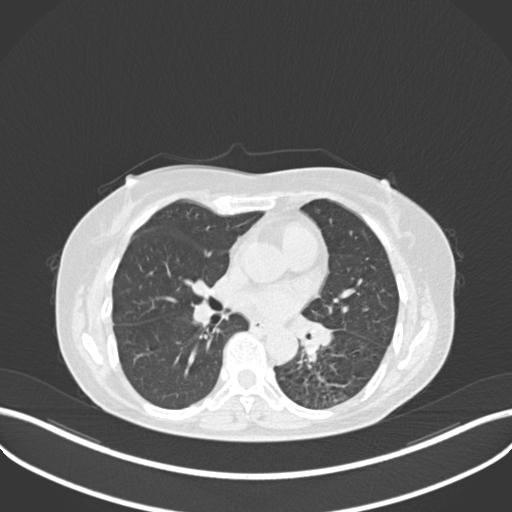
Chest CT, one axial slice; position 132 of 270 along the scan axis; reconstruction kernel B30f; 120 kVp; lung window (W 1500 / L -600 HU); 1 mm slice thickness; 512 × 512 image matrix. Female patient, age 63 years. From the clinical record (not read from this slice): clinical TNM (as recorded): T1b N0 M0; histopathological grade: G2-3.
Annotated regions visible in this slice (rectangle marked by the reading radiologist):
- lung tumour (recorded histology: adenocarcinoma): bounding box <294,313,331,360> (left, top, right, bottom; pixels)